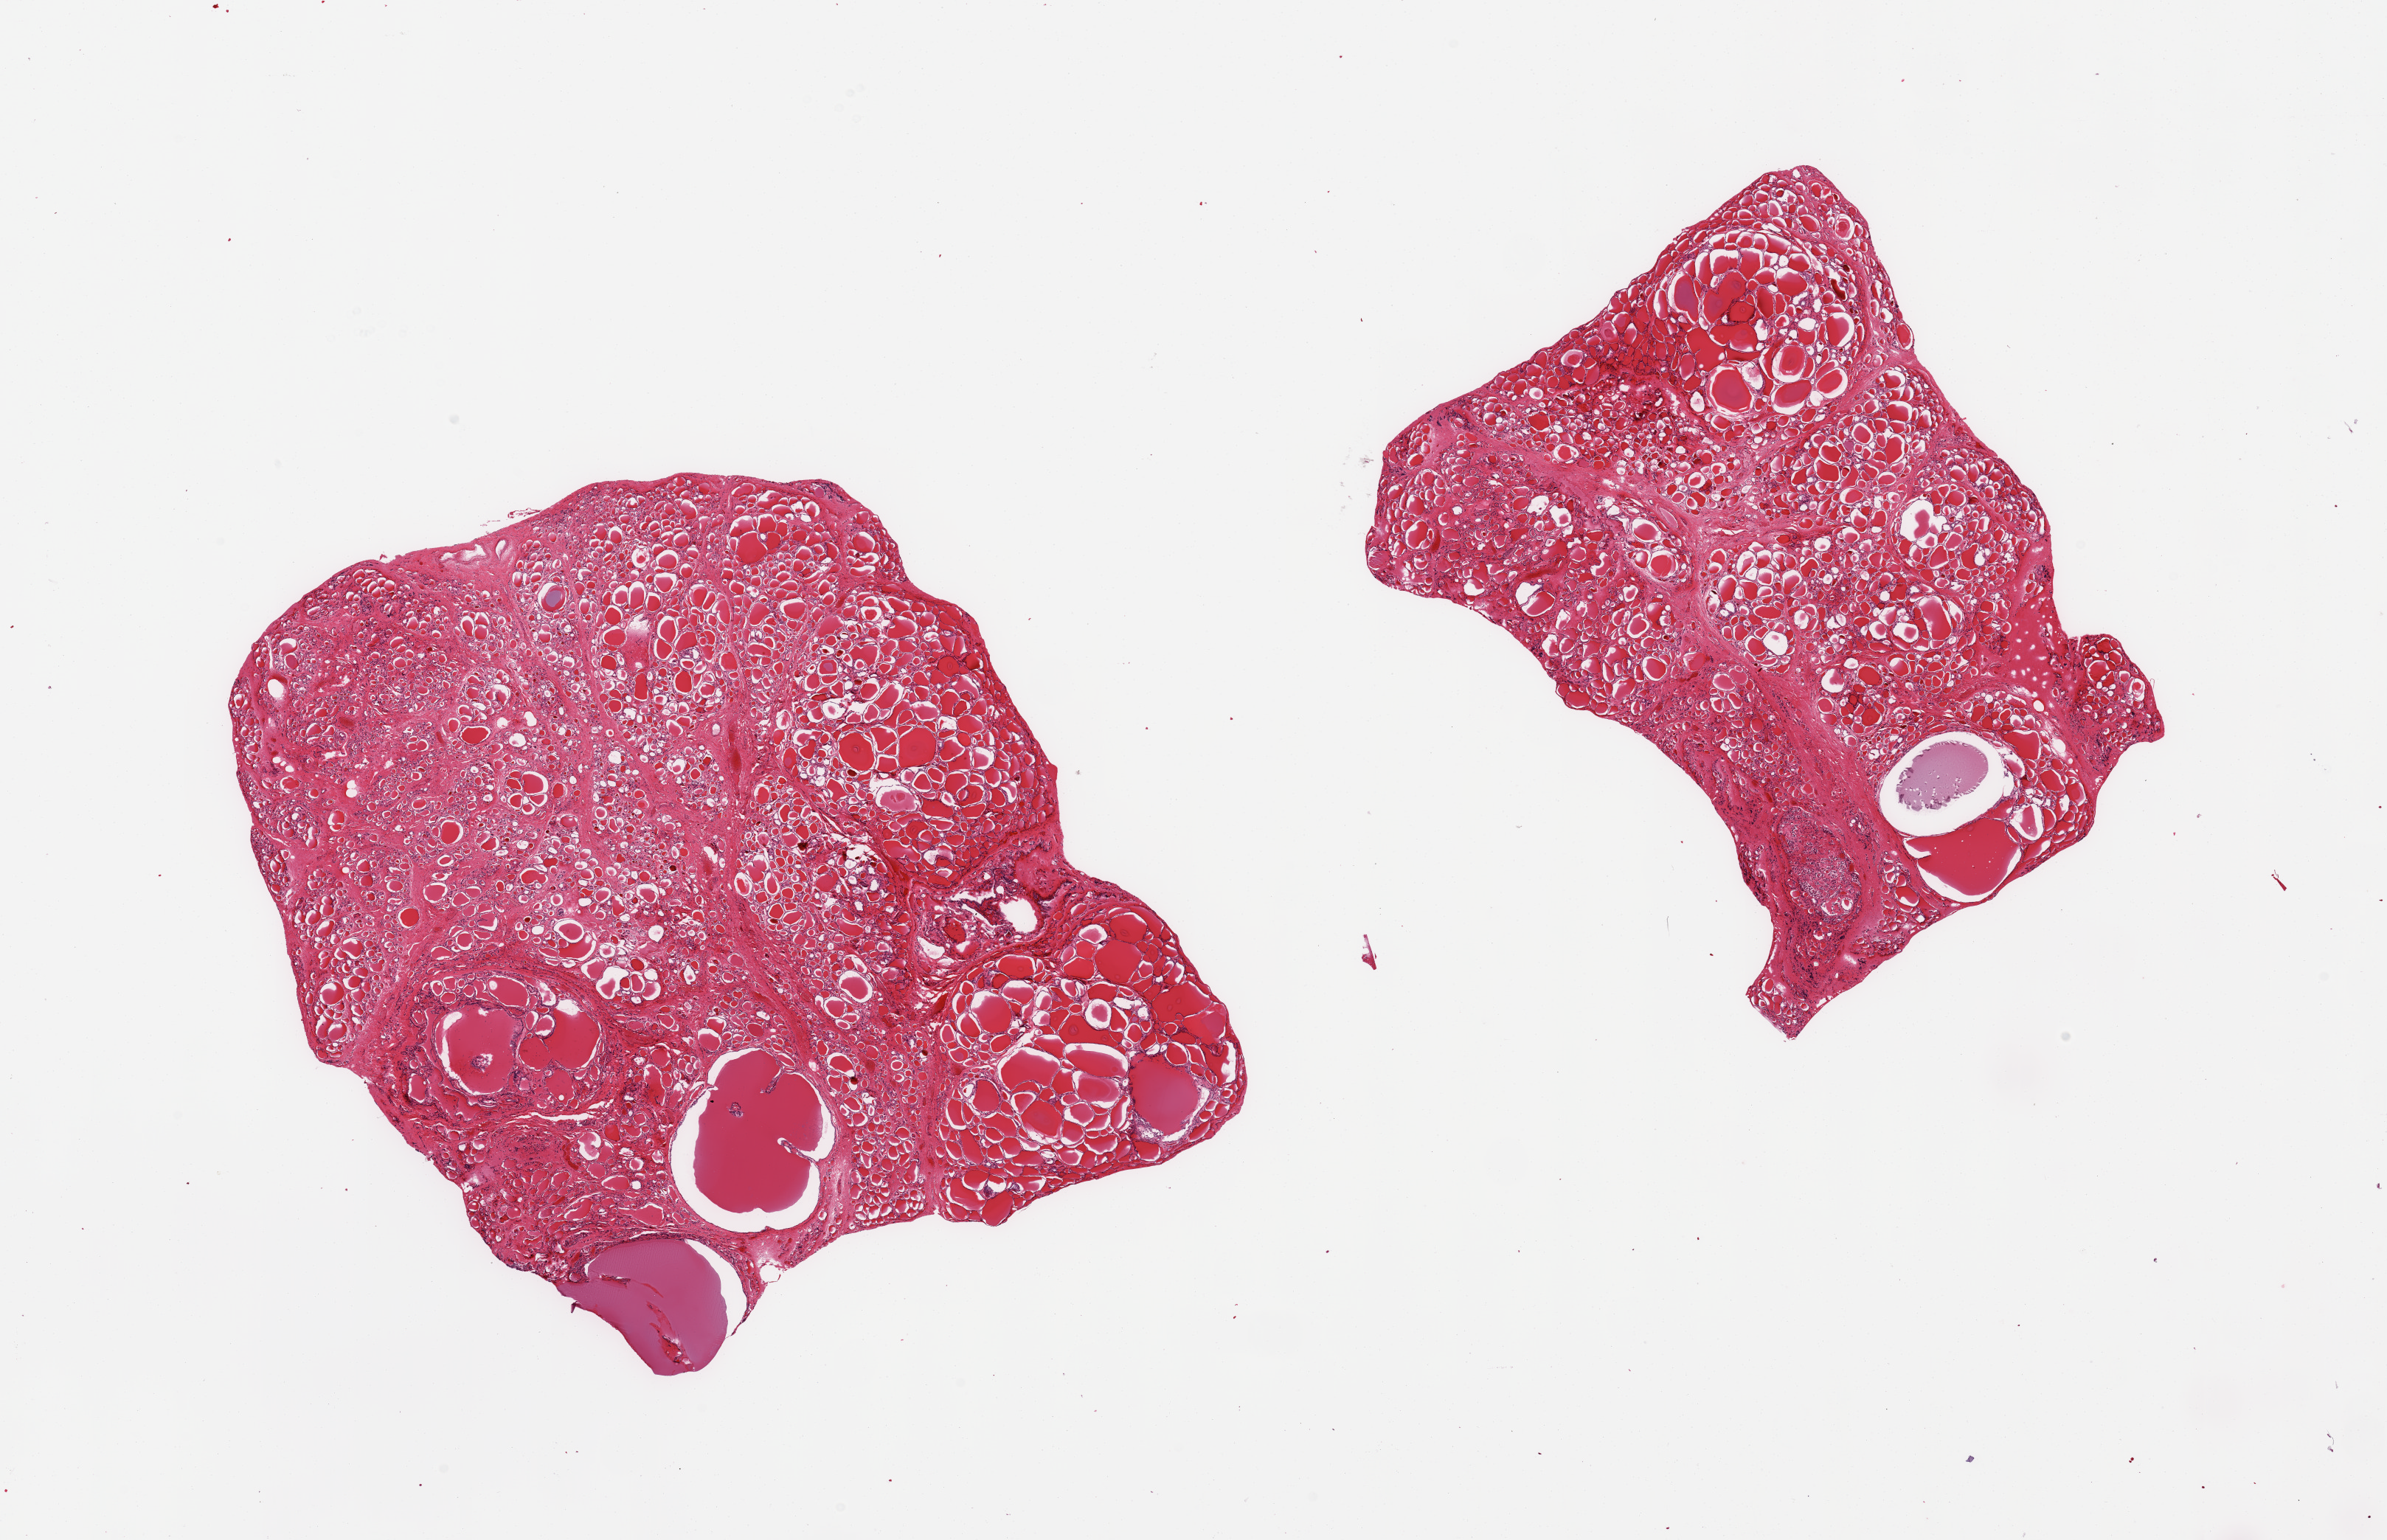
Whole-slide image, H&E stain, brightfield, whole scanned area (about 25.6 x 16.5 mm, slide scanned at 20x) shown as a low-resolution overview; PAXgene-fixed paraffin-embedded (PFPE) section; sampled site (target tissue): thyroid; tissue donor sample. Donor sex: female.
Reviewer comment on this tissue sample: 2 pieces; multinodular.